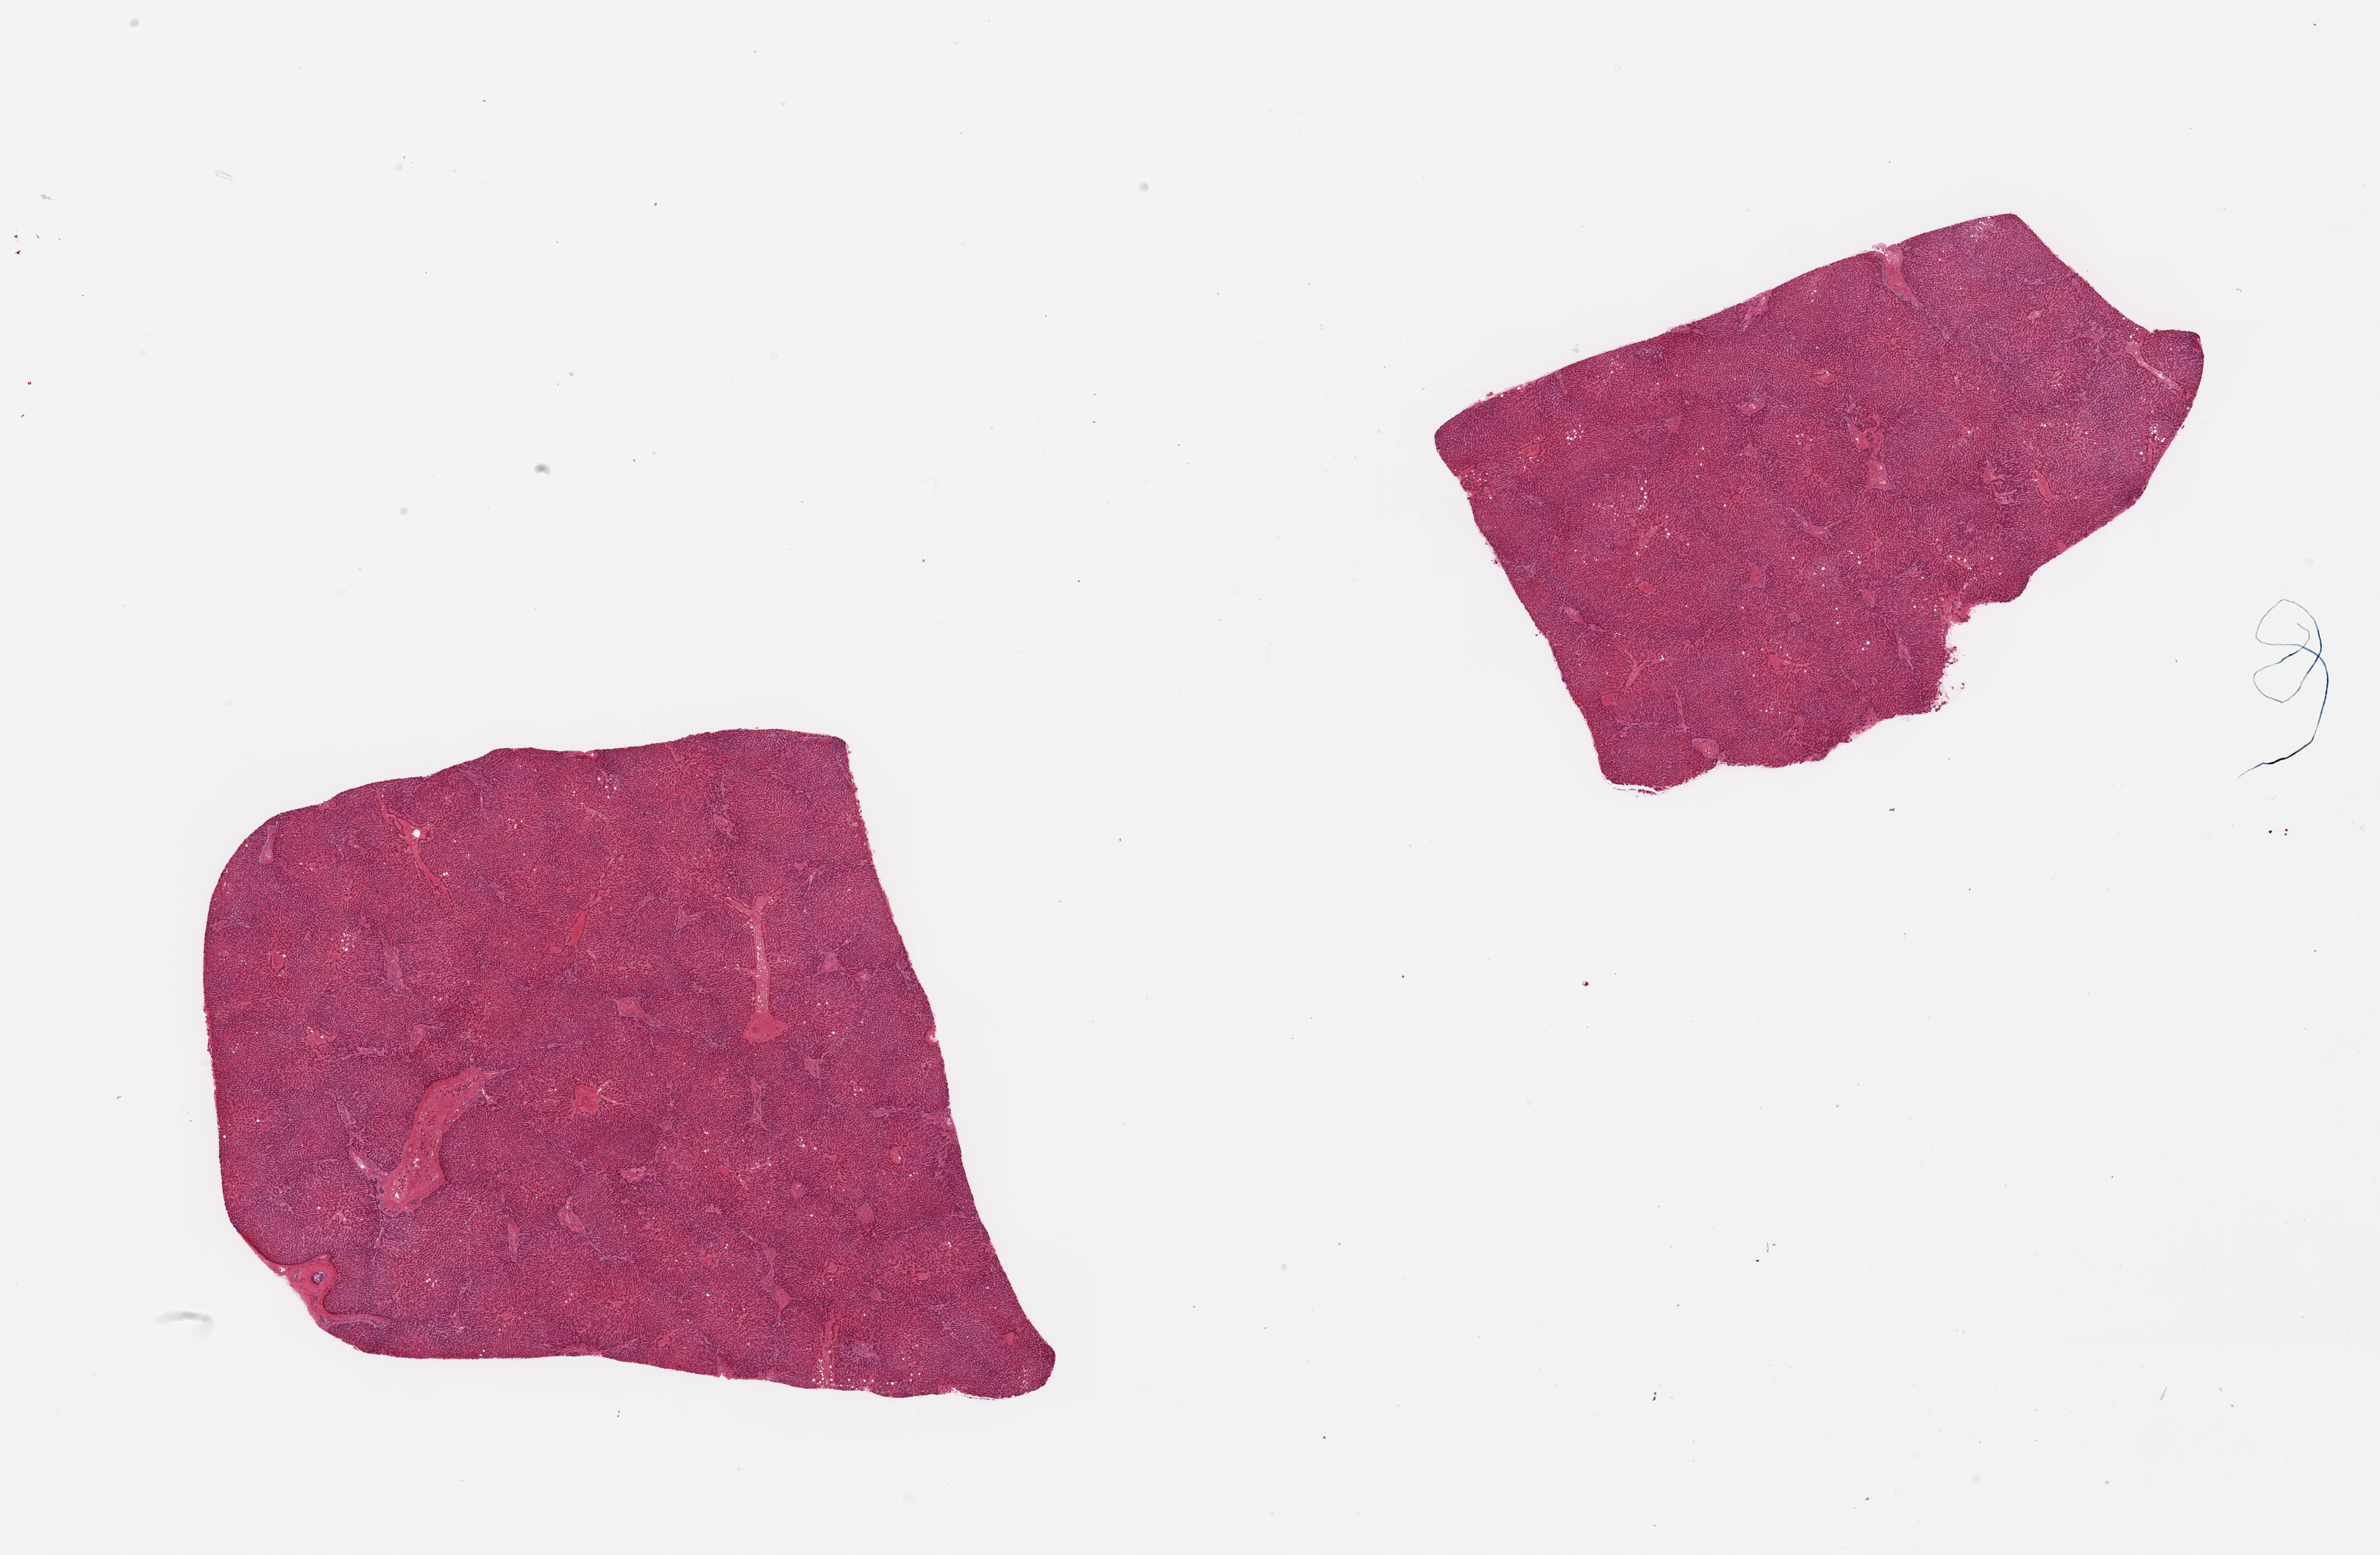
Whole-slide image, haematoxylin and eosin stain, brightfield, a low-resolution overview of the entire scanned area, about 25.6 x 16.7 mm. PAXgene-fixed paraffin-embedded (PFPE) section. Target tissue: liver. Tissue donor sample. Male donor.
* review note (as recorded): 2 pieces; mild microvesicular steatosis; marked congestion